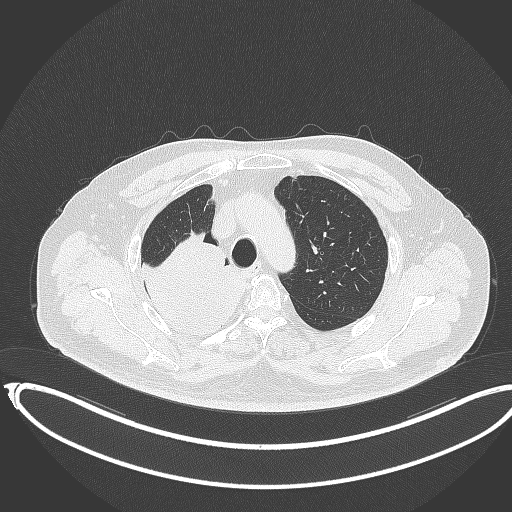
Chest CT, one axial slice; reconstruction kernel B70f; lung window (W 1500 / L -600 HU); 1 mm slice thickness; 512 × 512 image matrix, field of view 436 × 436 mm. Patient: male, 68 years. Case-level facts recorded for this patient, not image findings: clinical TNM (as recorded): T2a N0 M0.
Outlined on this slice (bounding box drawn by a radiologist):
- lung tumour (recorded histology: adenocarcinoma): bounding box <139,240,252,335> (left, top, right, bottom; pixels)